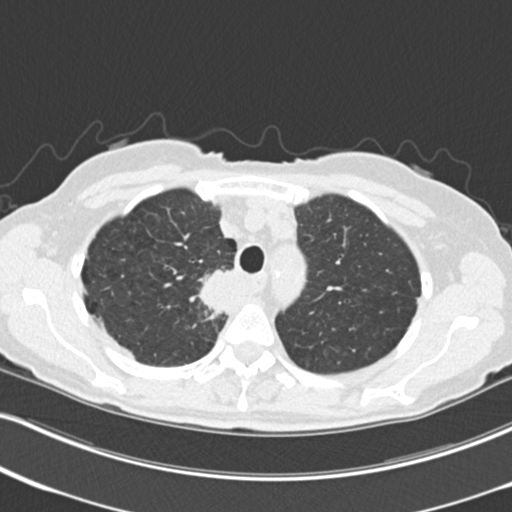
Chest CT (low-dose screening protocol), one axial image. Third annual screen. Lung window (W 1500 / L -600 HU). Standard (soft-tissue) reconstruction kernel (B30f). 120 kVp. 512 × 512 image matrix. Female participant, aged 68 years at enrolment.
• Expert reader's lesion annotation, bounding box <198,265,250,320> (left, top, right, bottom; pixels).
• Reader record for this screening exam (exam-level; its link to the box is not recorded): non-calcified nodule or mass ≥4 mm, right upper lobe, 31 × 29 mm, poorly defined margins, soft tissue attenuation, pre-existing on the prior screen: no.
• Participant outcome: lung cancer diagnosed 79 days after this screen — squamous cell carcinoma, NOS, right upper lobe, mediastinum, poorly differentiated (G3), stage IIIB (AJCC 6th edition), 43 mm at pathology.